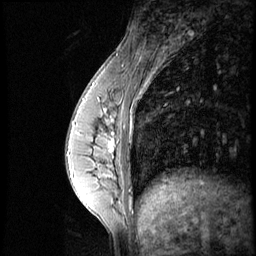
Breast MRI (dynamic contrast-enhanced), one sagittal slice. Slice 18 of 56 in the series (ordered by position). Dynamic contrast-enhanced series, image 2 of 4 at this slice position (ordered by acquisition). 1.5 T. TE 4.2 ms, TR 8.9 ms. 2.5 mm slice thickness. 256 × 256 image matrix, field of view 200 × 200 mm. Patient: female, 35 years. From the clinical record (not read from this slice): setting: breast cancer imaged before/during neoadjuvant chemotherapy; receptor status: HER2-positive.
Structures marked on this image (semi-automatic segmentation, software-assisted and operator-edited):
- analysis volume of interest (the breast-tissue region the enhancement analysis was run in; not a lesion): bounding box (x1, y1, x2, y2) in pixels: (73, 111, 131, 164)
- tumour enhancement mask (voxels above the 140 % enhancement threshold inside the analysis volume of interest): (74, 116, 115, 151)